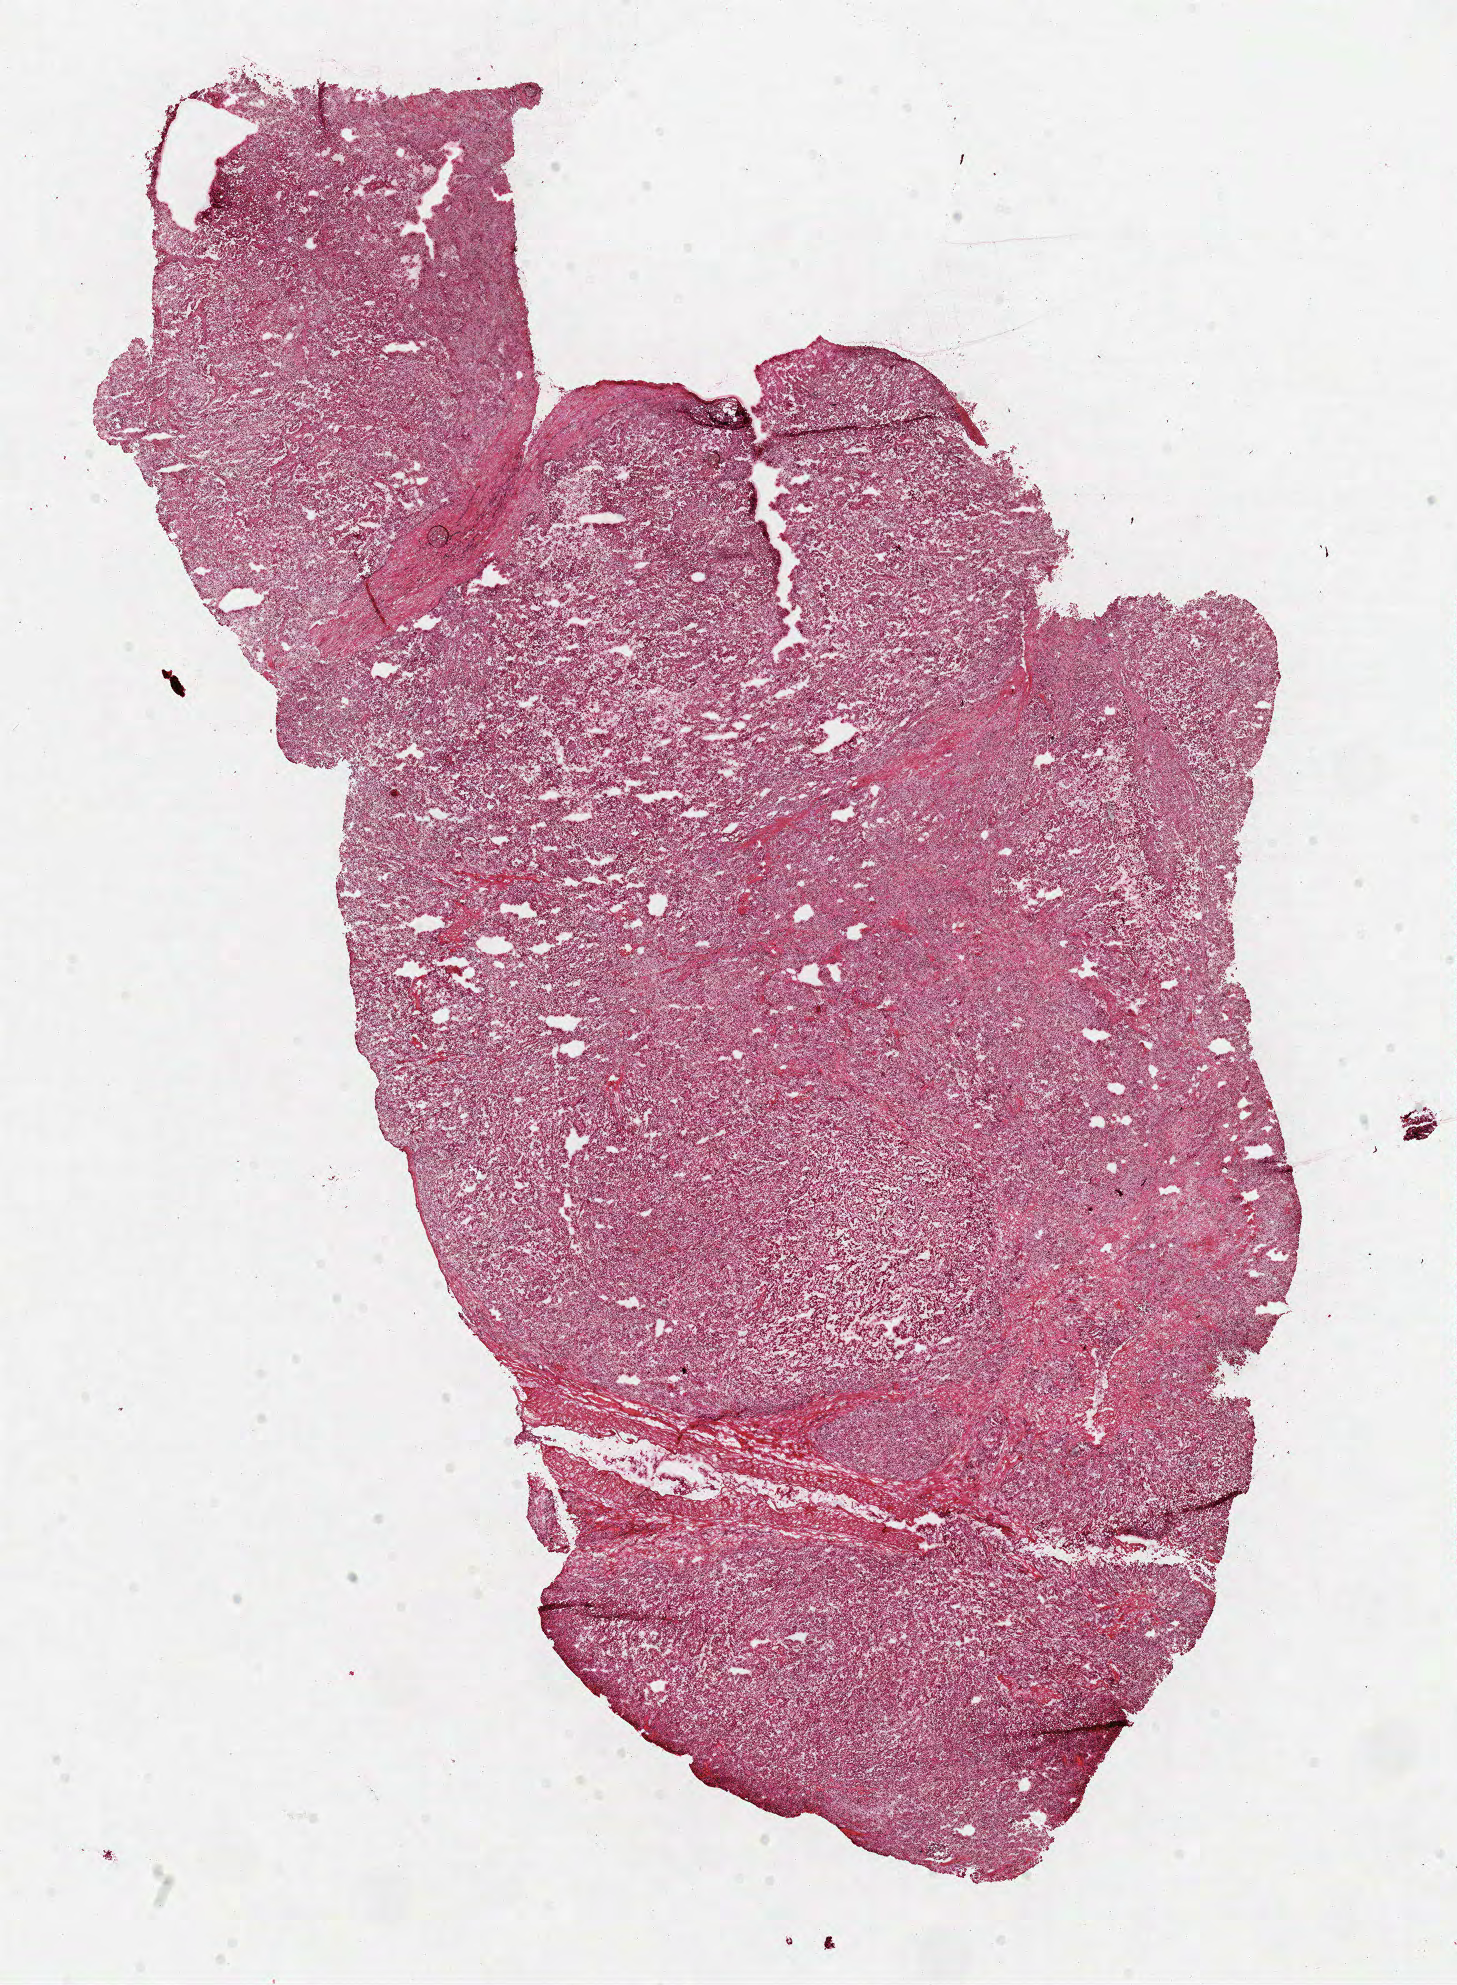
Digitized H&E-stained tissue section (whole slide) — shown as a low-resolution overview of the whole scanned area (about 11.5 x 15.6 mm, slide scanned at 40x), frozen section from the top of the tissue portion, sample: primary tumour, kidney. Male patient; age at initial diagnosis 60 years. Slide review estimates, as recorded: tumour cells 80%, tumour nuclei 80%, normal cells 0%, stromal cells 10%, necrosis 10%.
Laterality: left. Histologic diagnosis: Papillary adenocarcinoma, NOS. AJCC pathologic stage: IV.